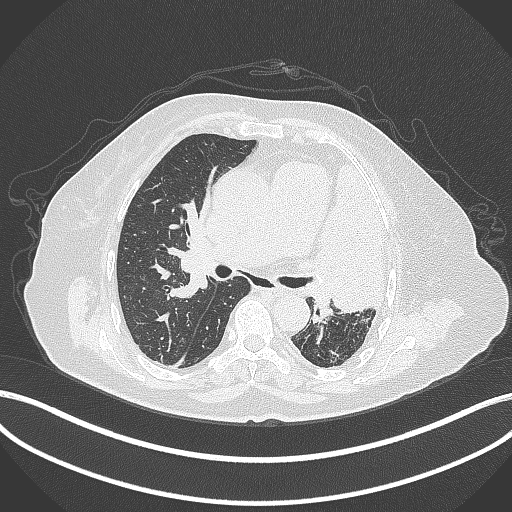
Chest CT, one axial slice. Reconstruction kernel B70f. 120 kVp. Lung window (W 1500 / L -600 HU). 512 × 512 image matrix, field of view 400 × 400 mm. Patient: female, 75 years. From the clinical record (not read from this slice): clinical TNM (as recorded): T3 N3 M1.
Annotated regions visible in this slice (bounding box drawn by a radiologist):
- lung tumour (recorded histology: adenocarcinoma): bounding box <303,157,396,318> (left, top, right, bottom; pixels)